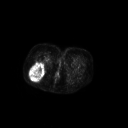
FDG PET of an extremity soft-tissue mass (from a PET/CT study), one axial slice. Position 47 of 267 along the scan axis. 3.27 mm slice thickness. 128 × 128 image matrix. Female patient, age 70 years. From the clinical record (not read from this slice): histological type: synovial sarcoma; grade: intermediate; site of the primary tumour: right buttock.
Structures marked on this image (expert contour drawn on MRI and transferred to this co-registered scan by the dataset authors):
- gross tumour volume including surrounding oedema: box from (x=29, y=62) to (x=45, y=81) px
- gross tumour volume (mass): (x=29, y=62)–(x=45, y=81)